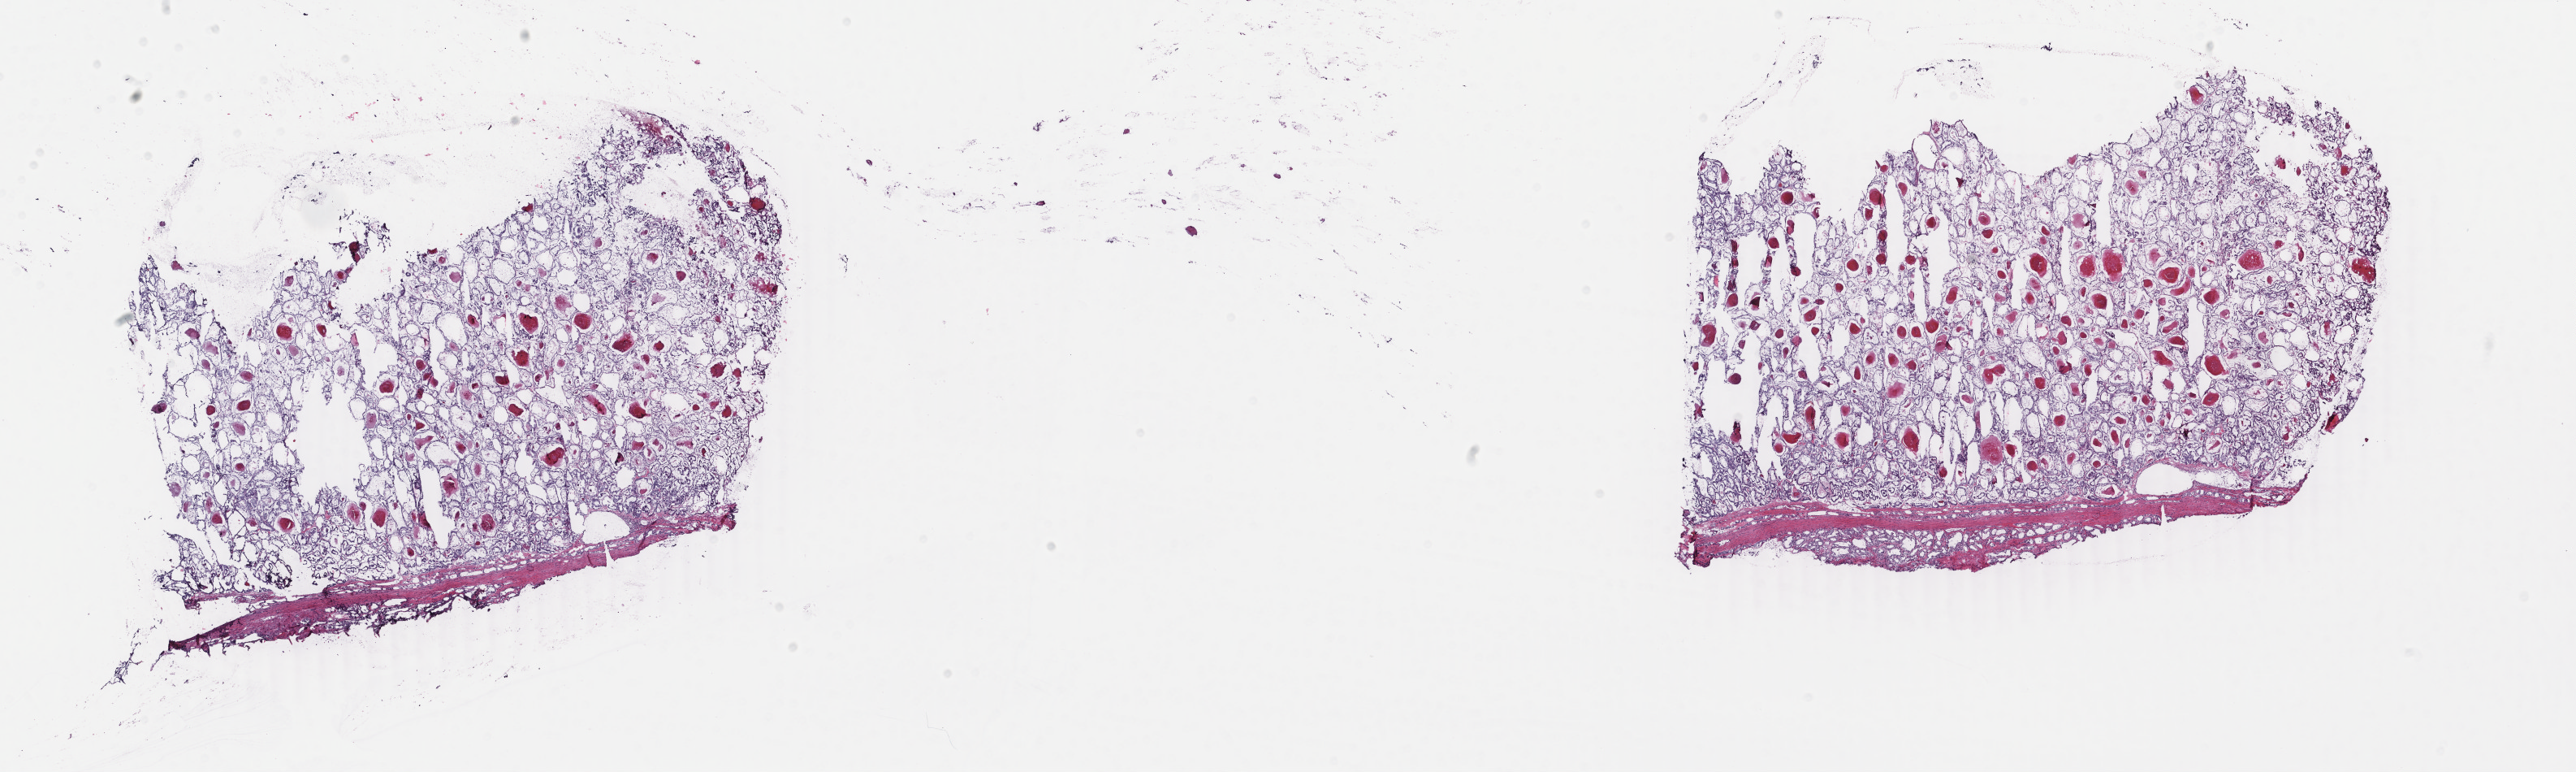
Hematoxylin and eosin (H&E) stained whole-slide image — shown as a low-resolution overview of the whole scanned area (about 25.2 x 7.6 mm, from a 40x scan), frozen section, sample: primary tumour, thyroid. Female, age 51 years at initial diagnosis. Composition of this section per pathologist review: tumour cells 90%, tumour nuclei 85%, normal cells 5%, stromal cells 5%, necrosis 0%. Inflammatory infiltration, as recorded: lymphocyte infiltration 0%, monocyte infiltration 0%, neutrophil infiltration 0%.
• histologic diagnosis: Papillary carcinoma, follicular variant (thyroid gland)
• AJCC pathologic stage: III
• lymph nodes positive (case pathology): 0 of 1 examined
• TNM: T3 N0 M0